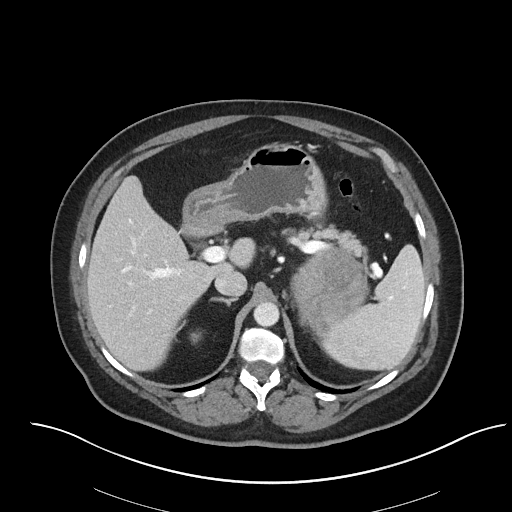
Contrast-enhanced abdominal CT, one axial slice; reconstruction kernel I40f/2; intravenous contrast given; soft-tissue window (W 400 / L 40 HU); 3 mm slice thickness; 512 × 512 image matrix, field of view 440 × 440 mm. Female patient, age 53 years. Case-level facts recorded for this patient, not image findings: diagnosis: adrenocortical carcinoma; tumour side: left adrenal; tumour size at pathology: 9 cm; Ki-67 index: 28 %; stage (as recorded): 2.
Outlined on this slice (semi-automatic segmentation, software-assisted and operator-edited):
- mass: box from (x=292, y=251) to (x=365, y=334) px